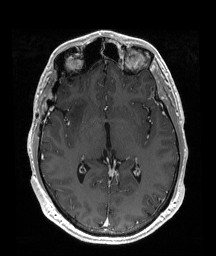
Brain MRI from a brain-tumour surgery series, one axial slice. Position 106 of 192 along the scan axis. T1-weighted post-contrast. 1 mm slice thickness. 216 × 256 image matrix, field of view 219 × 260 mm. From the clinical record (not read from this slice): histopathology: Astrocytoma; WHO grade: 2; IDH mutation: yes; tumour location: Right Insular.
Outlined on this slice (outlined manually by an expert reader):
- tumour: bounding box <70,94,91,131> (left, top, right, bottom; pixels)